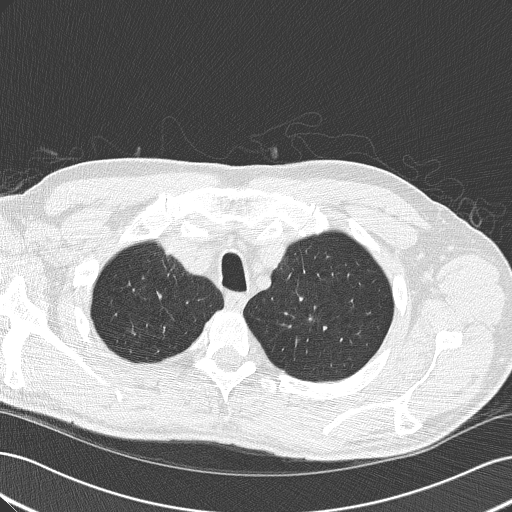
Low-dose screening chest CT, one axial slice. Position 155 of 189 along the scan axis. Reconstruction kernel B50f. Lung window (W 1500 / L -600 HU). 512 × 512 image matrix.
Outlined on this slice (outlined manually by an expert reader):
- lesion 1 (tumor, upper lobe of left lung): box from (x=309, y=308) to (x=316, y=323) px